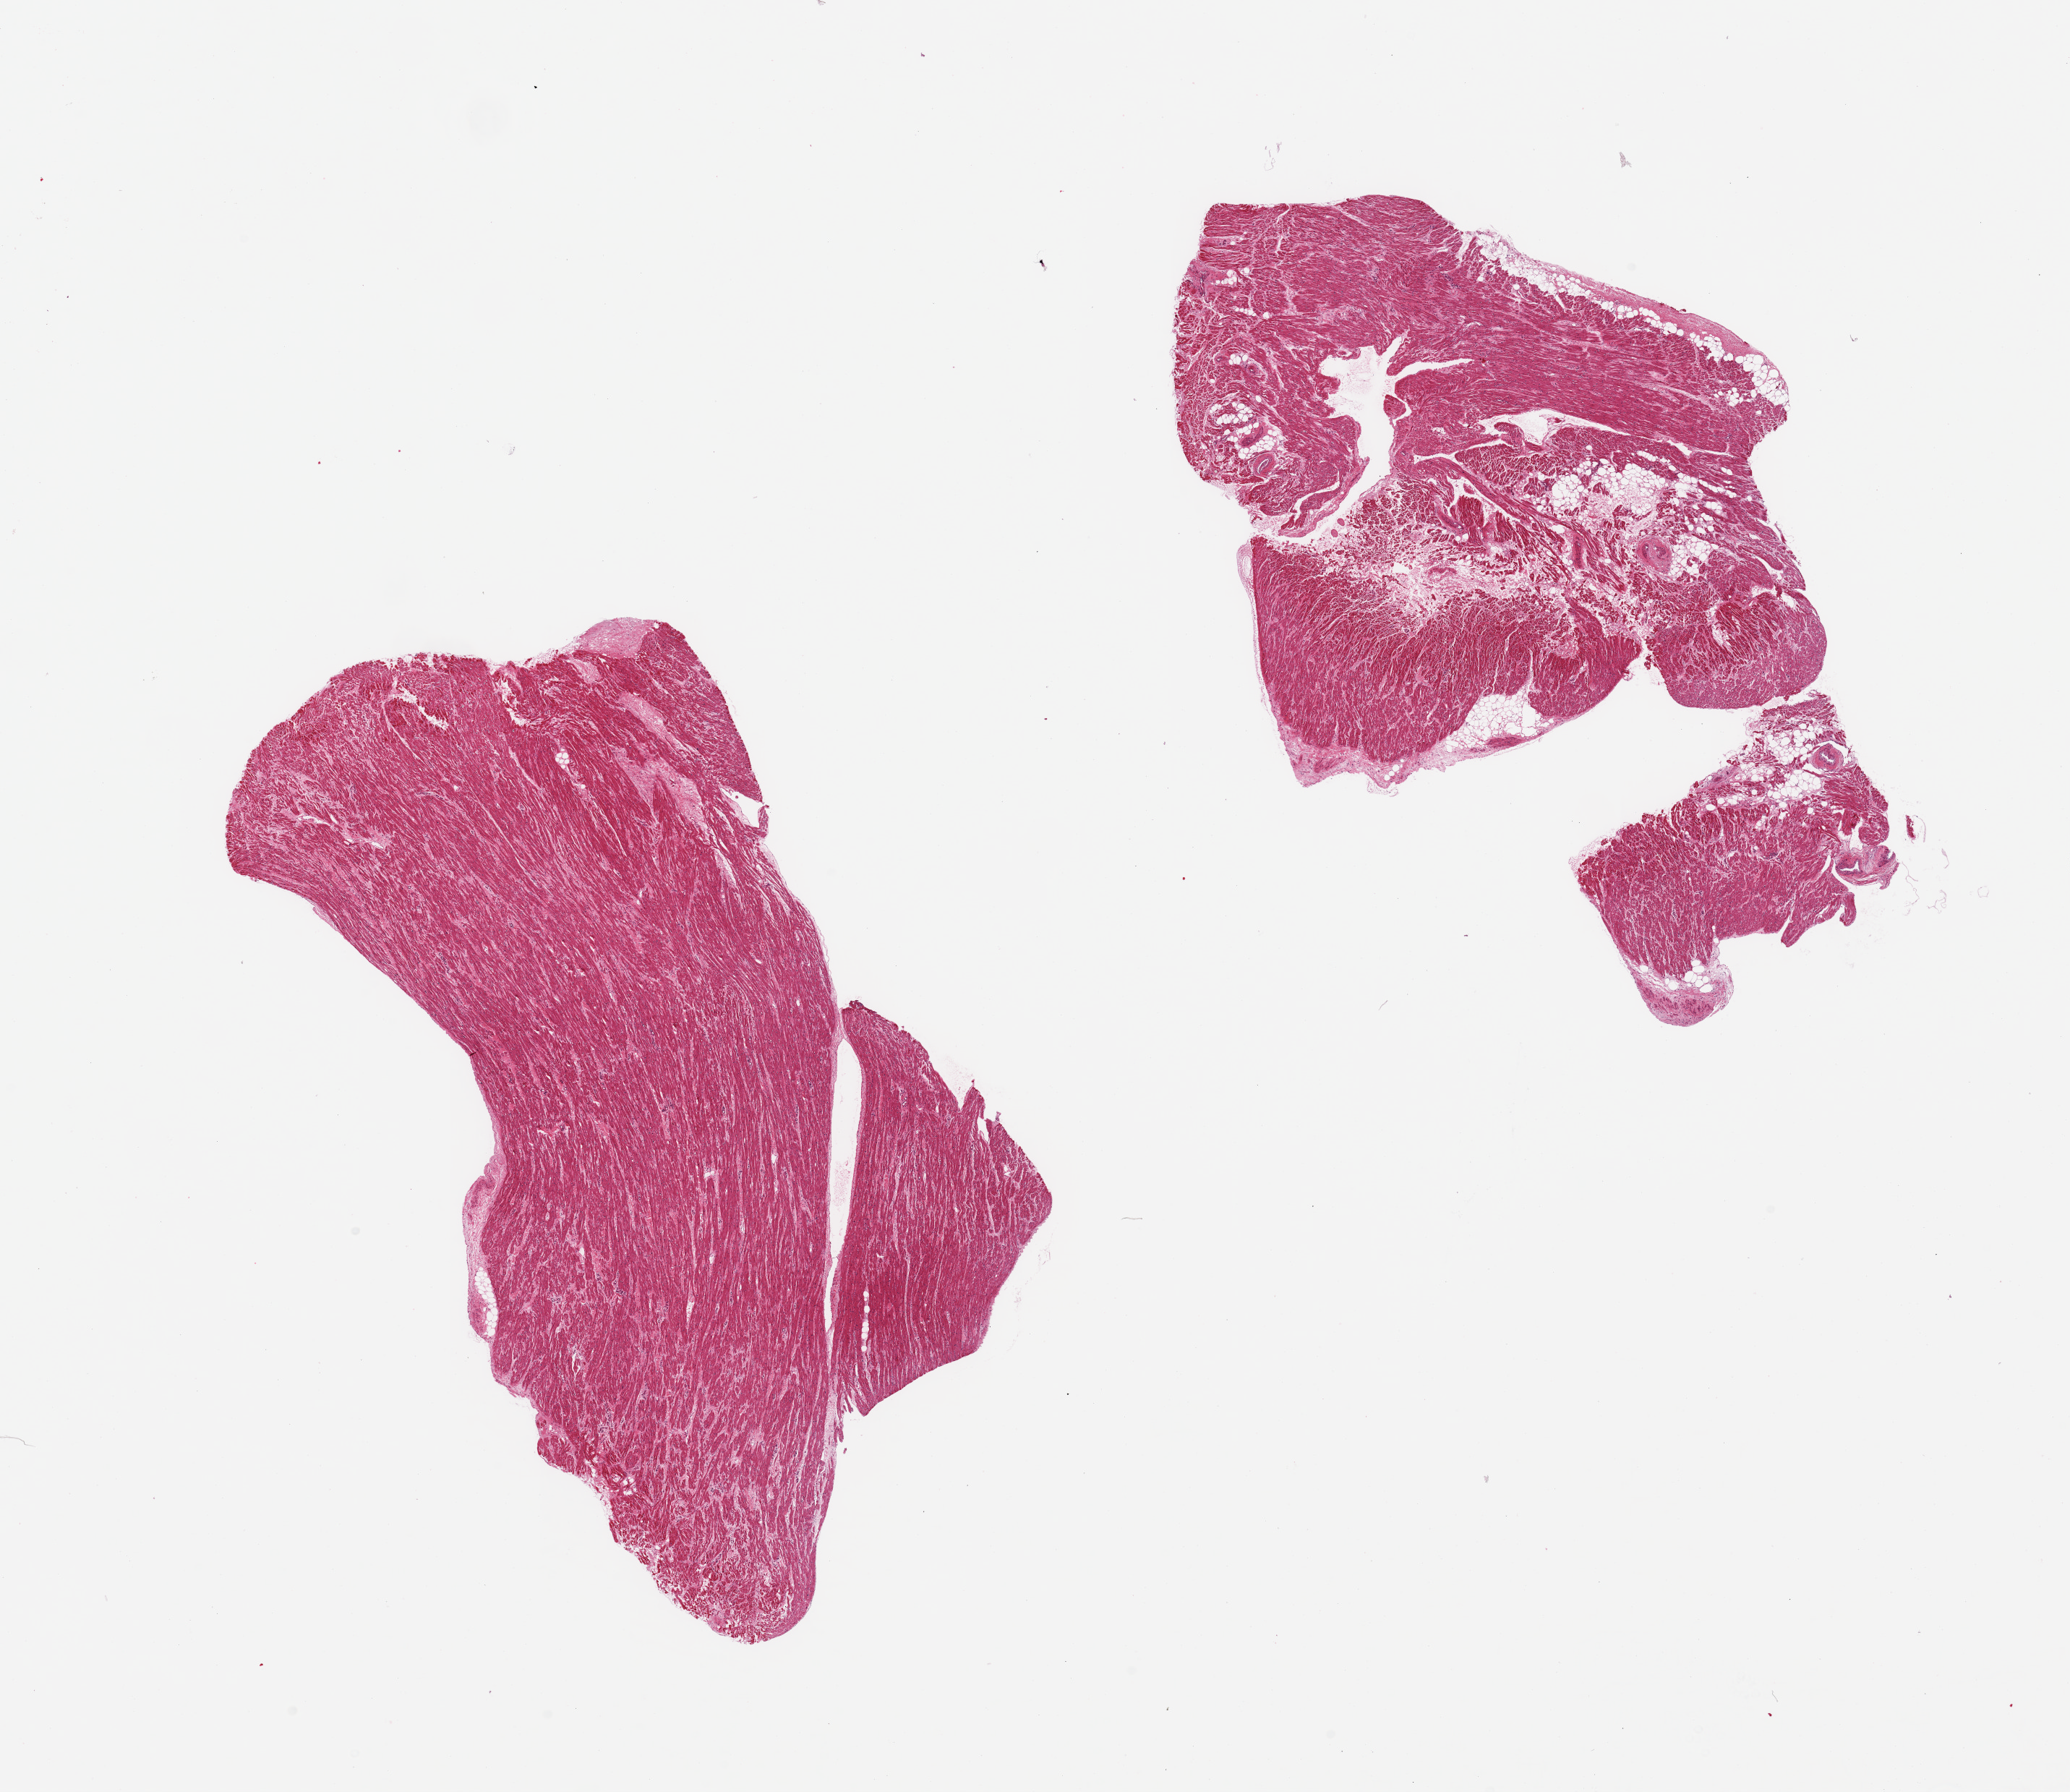
Hematoxylin and eosin (H&E) whole-slide image — shown as a low-resolution overview of the whole scanned area (about 22.6 x 19.6 mm, slide scanned at 20x); PAXgene-fixed paraffin-embedded (PFPE) section; target tissue: auricular appendage; tissue donor sample. Donor: female.
Pathologist's review note for this sample: 2 pieces; one well trimmed fibromuscular tissue and other with ~15% internal/external fat.